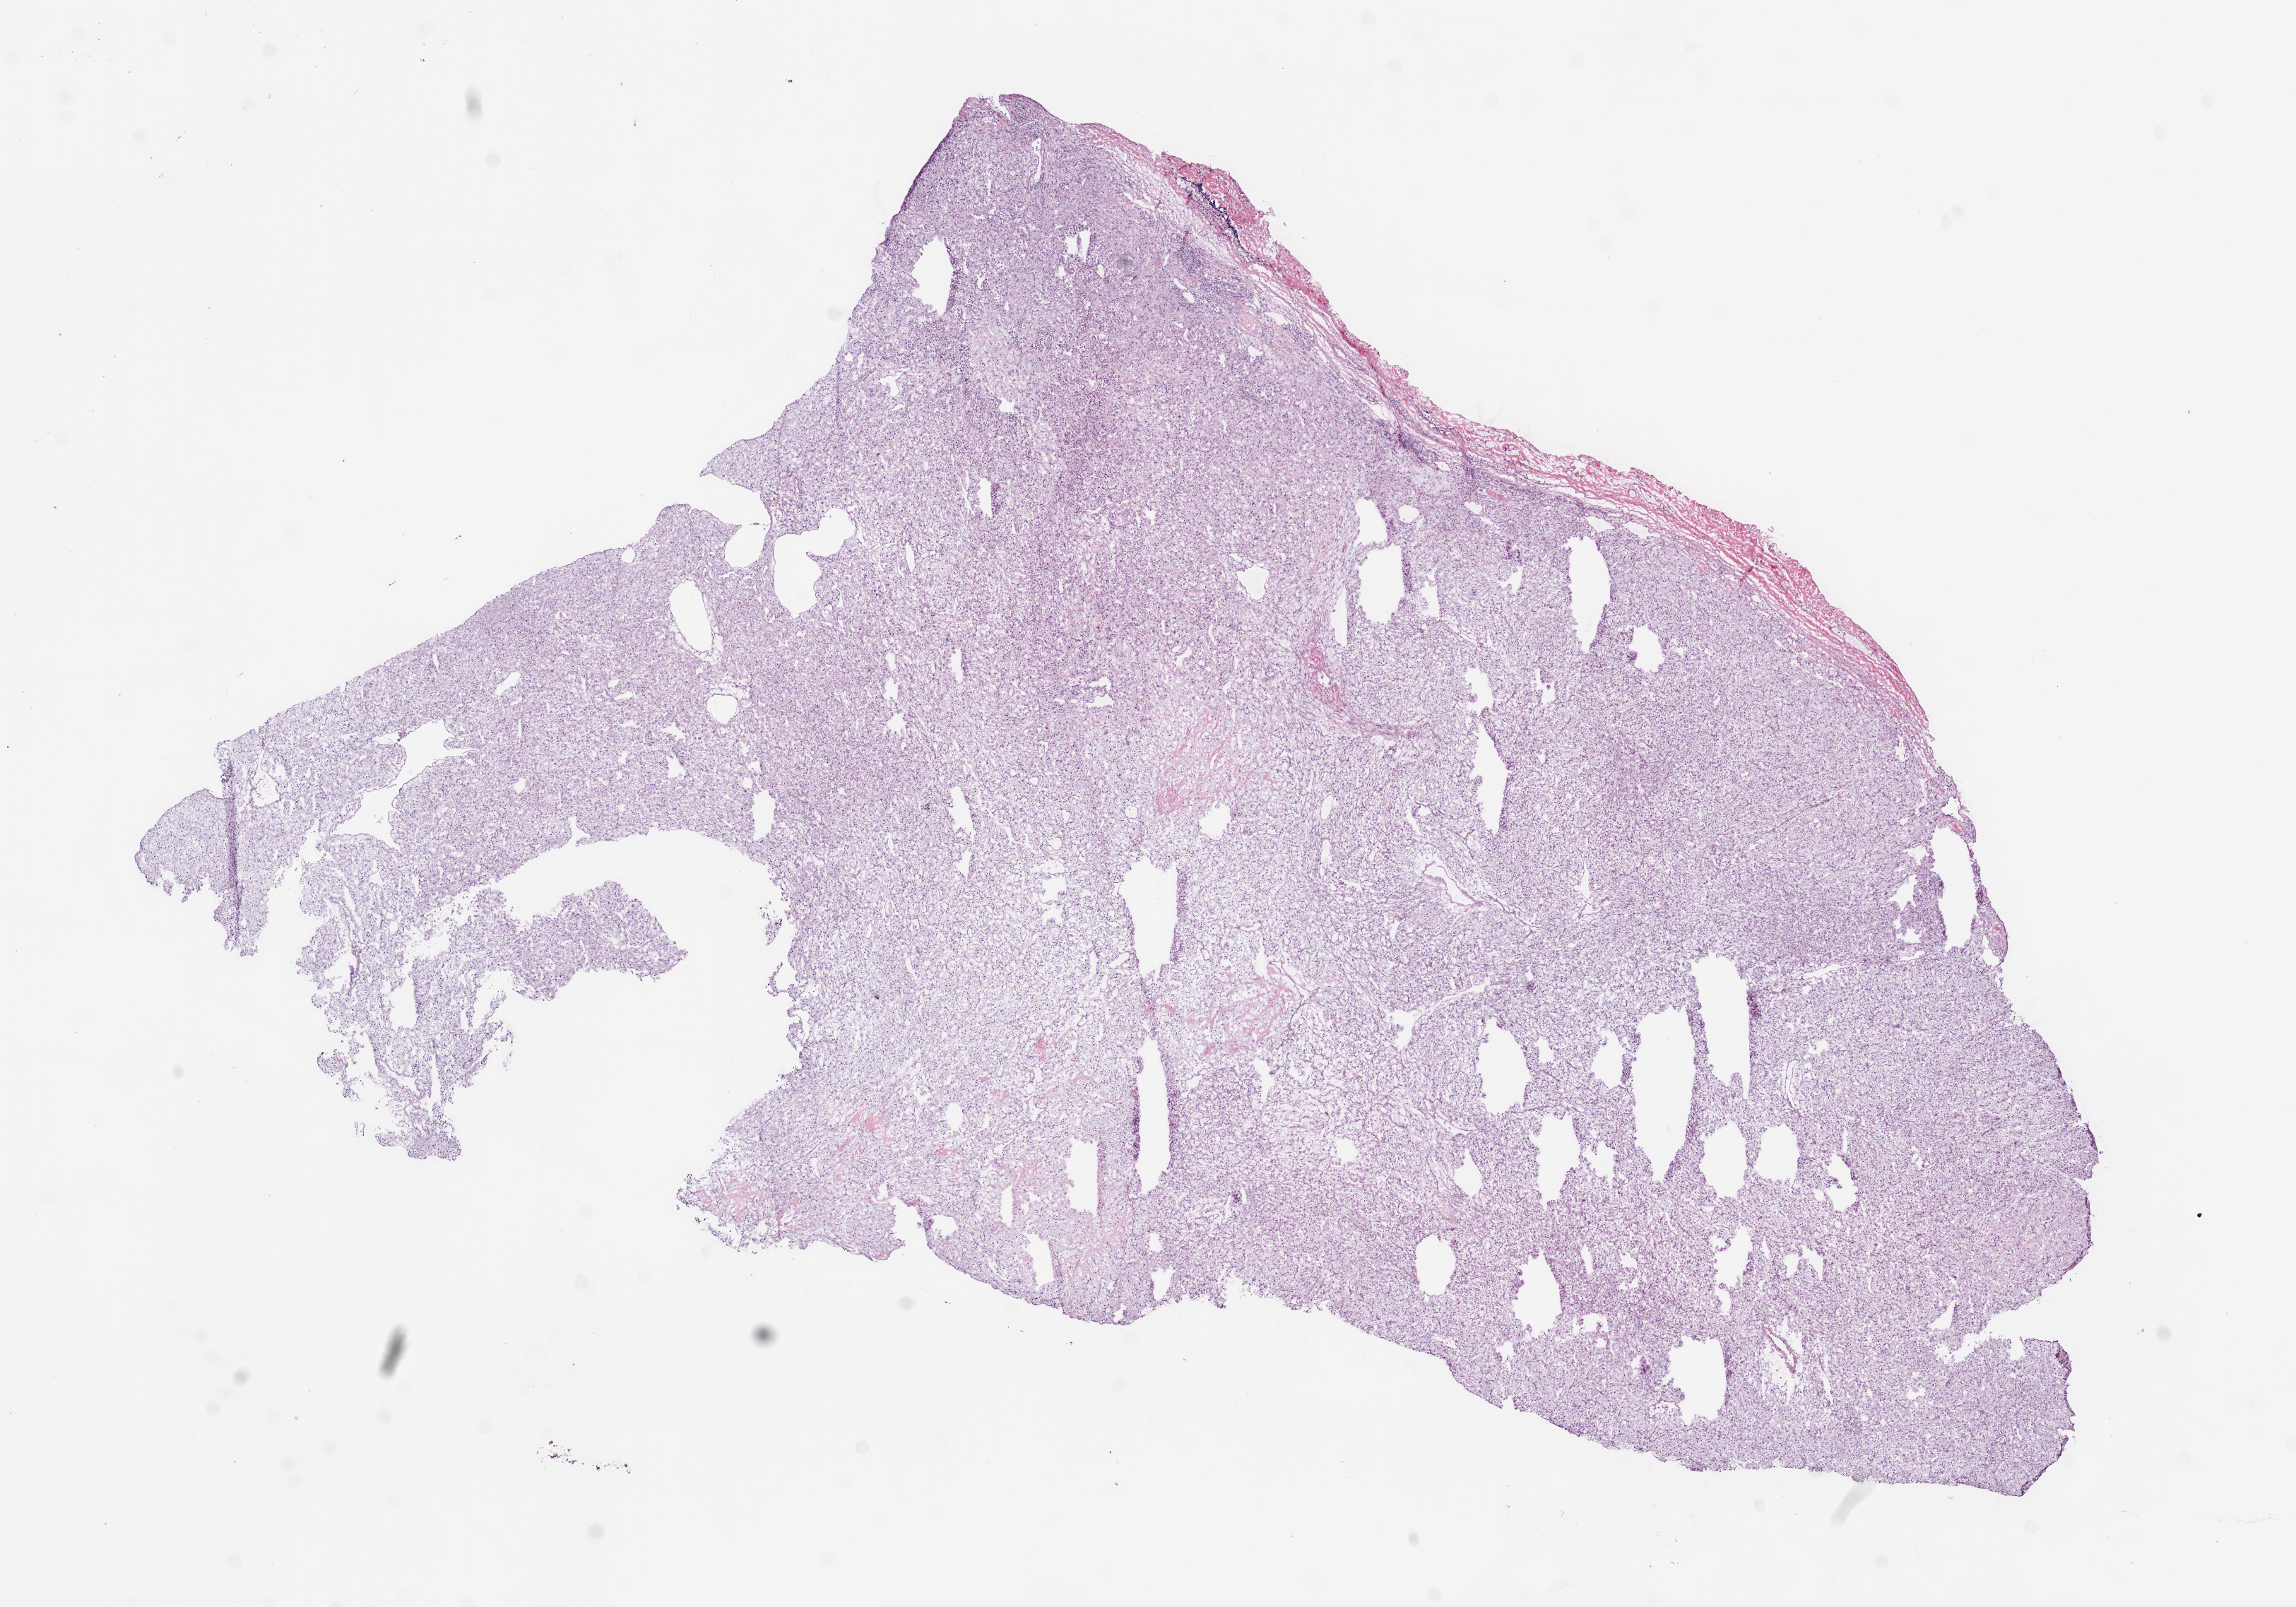
Digitized H&E tissue section (whole slide) — shown as a low-resolution overview of the whole scanned area (about 13.0 x 9.1 mm, acquisition: 20x scan). Frozen section from the bottom of the tissue portion. Kidney, primary tumour sample. Patient: male, age at initial diagnosis 75 years. Histologic grade: G3 (poorly differentiated). Pathologist review of this section (percent, as recorded): tumour cells 90%, tumour nuclei 85%, normal cells 0%, stromal cells 10%, necrosis 0%.
TNM: T1a N0 M0. AJCC pathologic stage: I. Lymph nodes positive (case pathology): 0 of 4 examined. Diagnosis: Clear cell adenocarcinoma, NOS.